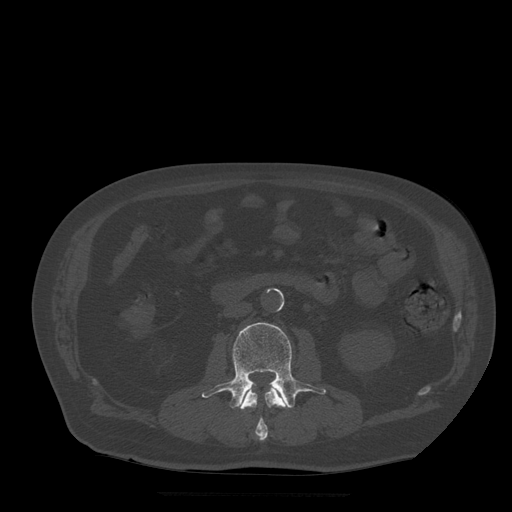
CT including the spine, one axial slice. Position 149 of 522 along the scan axis. Bone window (W 1800 / L 400 HU). 512 × 512 image matrix, field of view 420 × 420 mm. Patient age 72 years. Case-level facts recorded for this patient, not image findings: primary cancer: prostate.
Outlined on this slice (semi-automatic segmentation, software-assisted and operator-edited):
- L2 vertebra: bounding box <240,385,288,441> (left, top, right, bottom; pixels)
- L3 vertebra: <202,323,326,409>